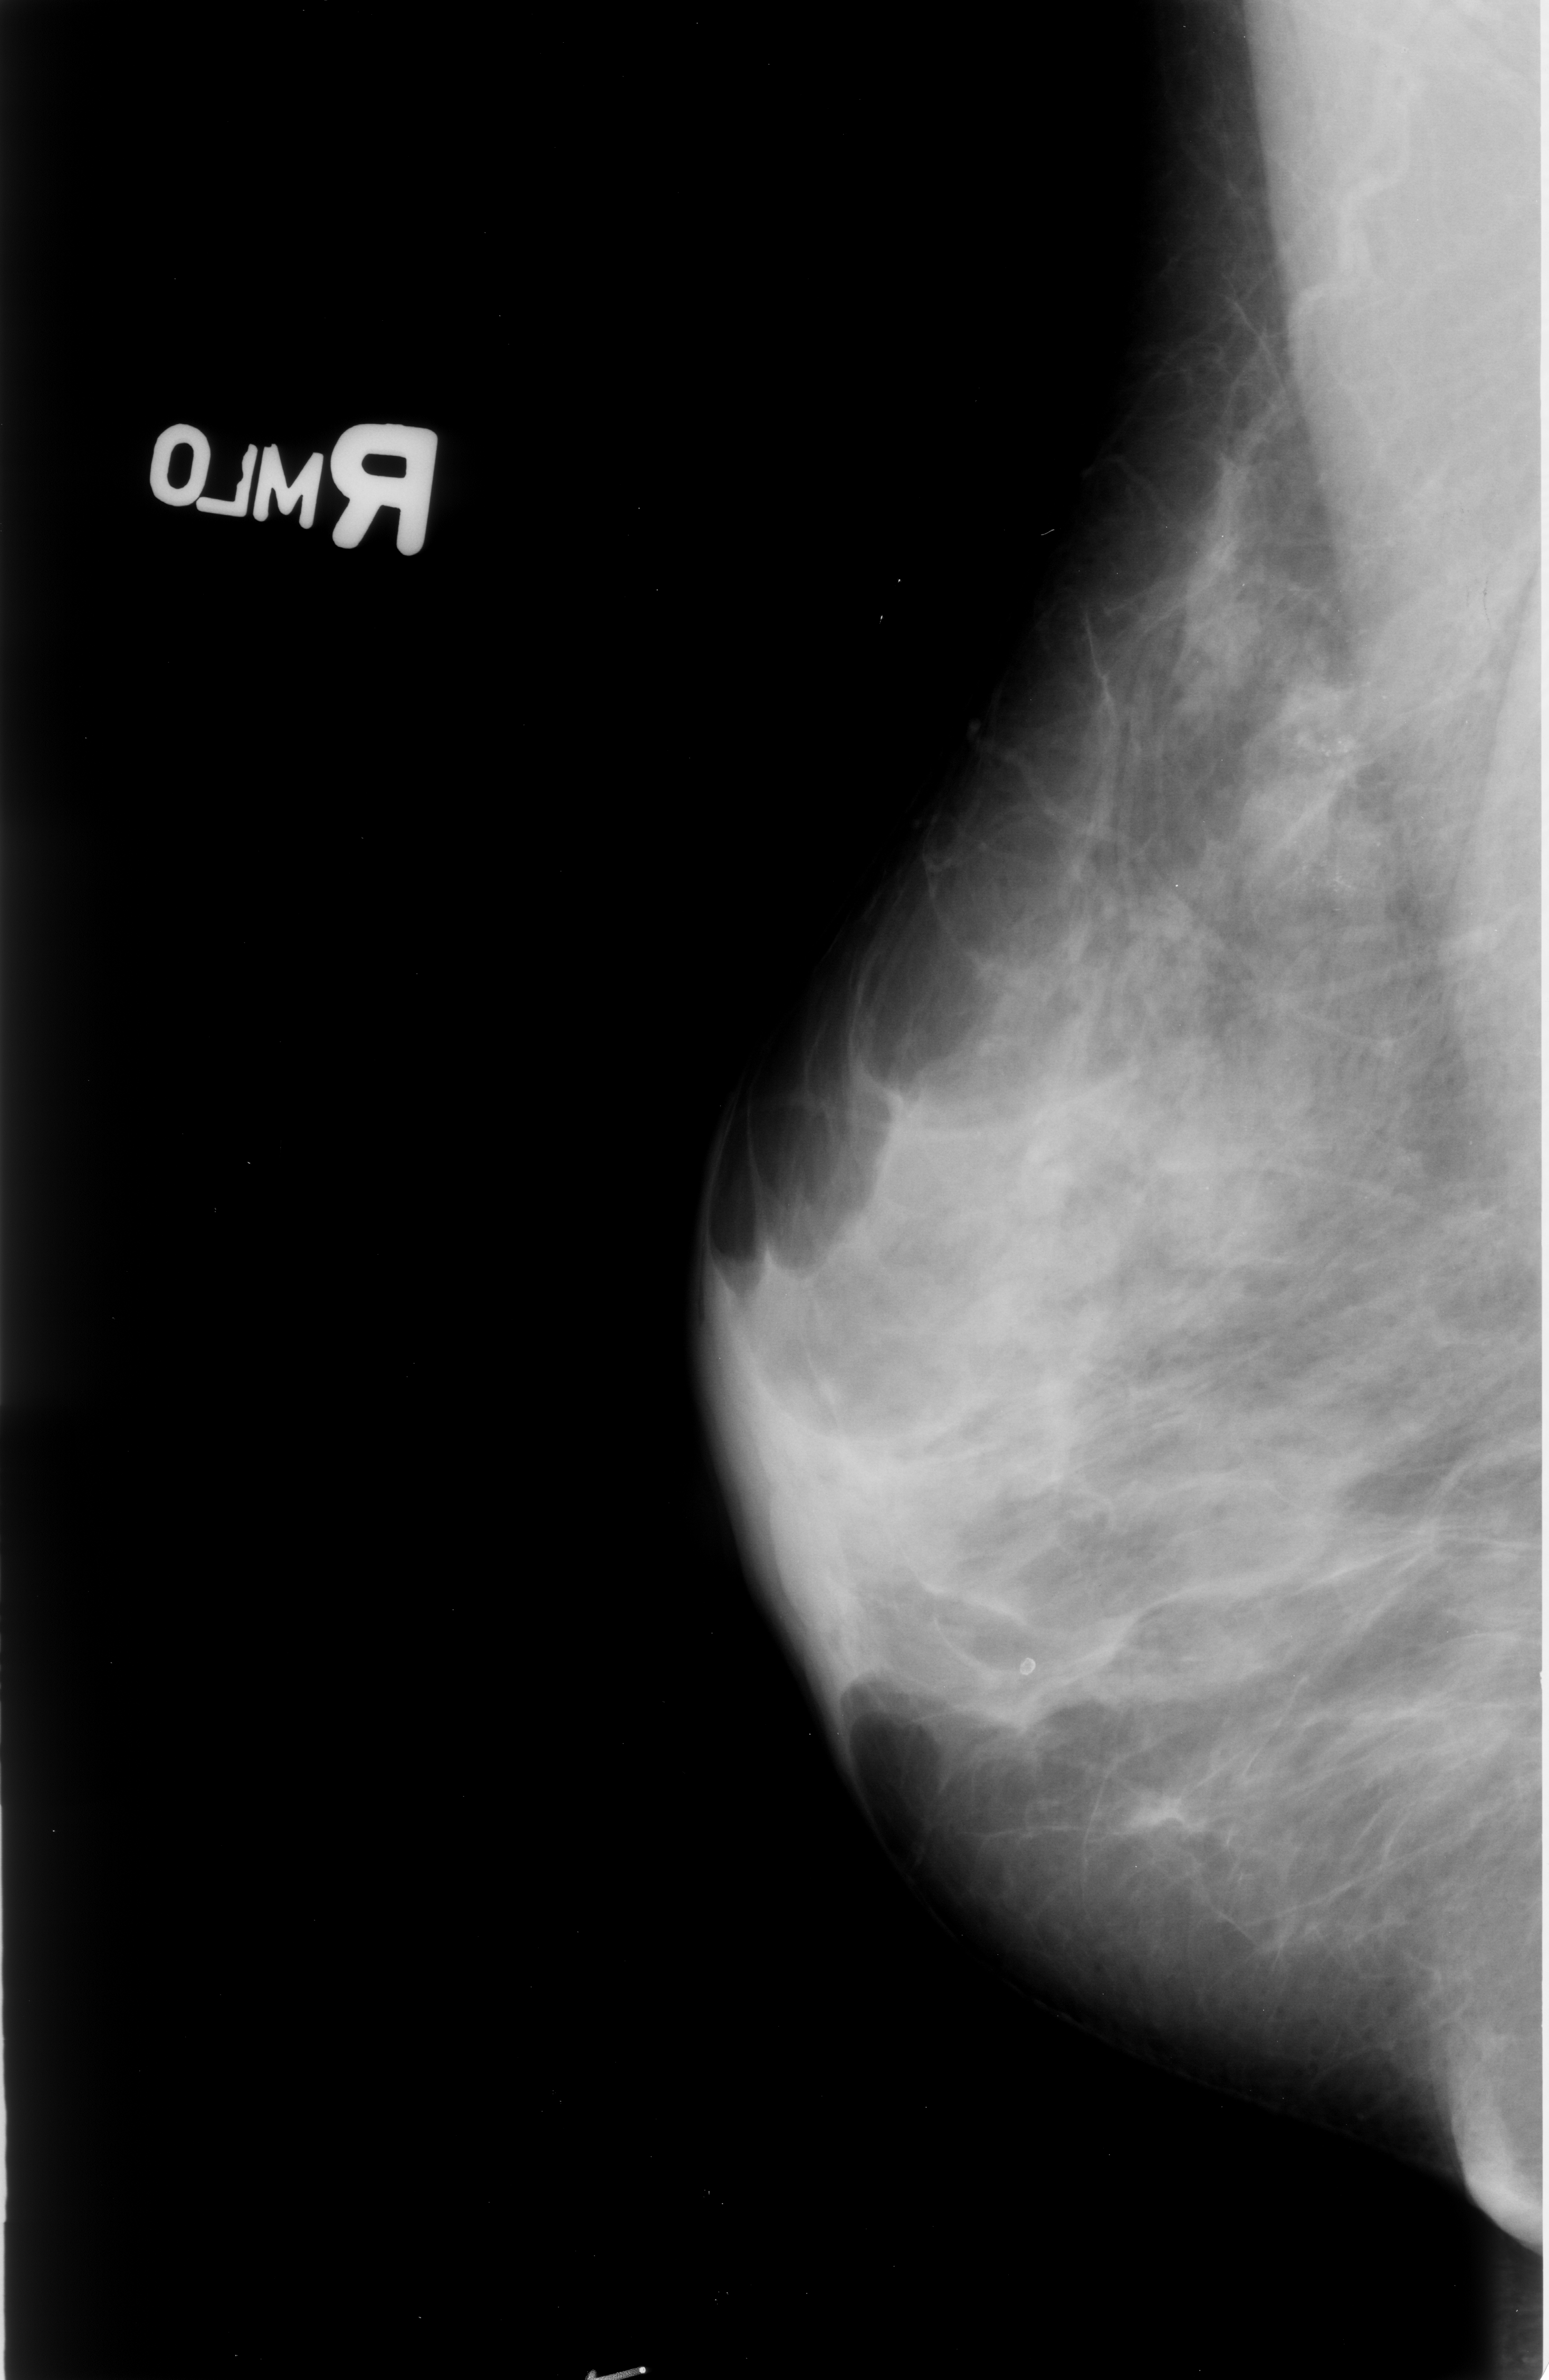
Digitized screen-film mammogram. Right breast. Mediolateral oblique (MLO) view. BI-RADS breast density category 3 (scale 1–4). 1549 × 2380 image matrix.
Expert-marked regions of interest on this film, with their recorded descriptors:
- calcifications, morphology punctate / pleomorphic, distribution clustered; BI-RADS assessment category 4; pathology (as recorded): malignant: bounding box <1202,540,1533,950> (left, top, right, bottom; pixels)